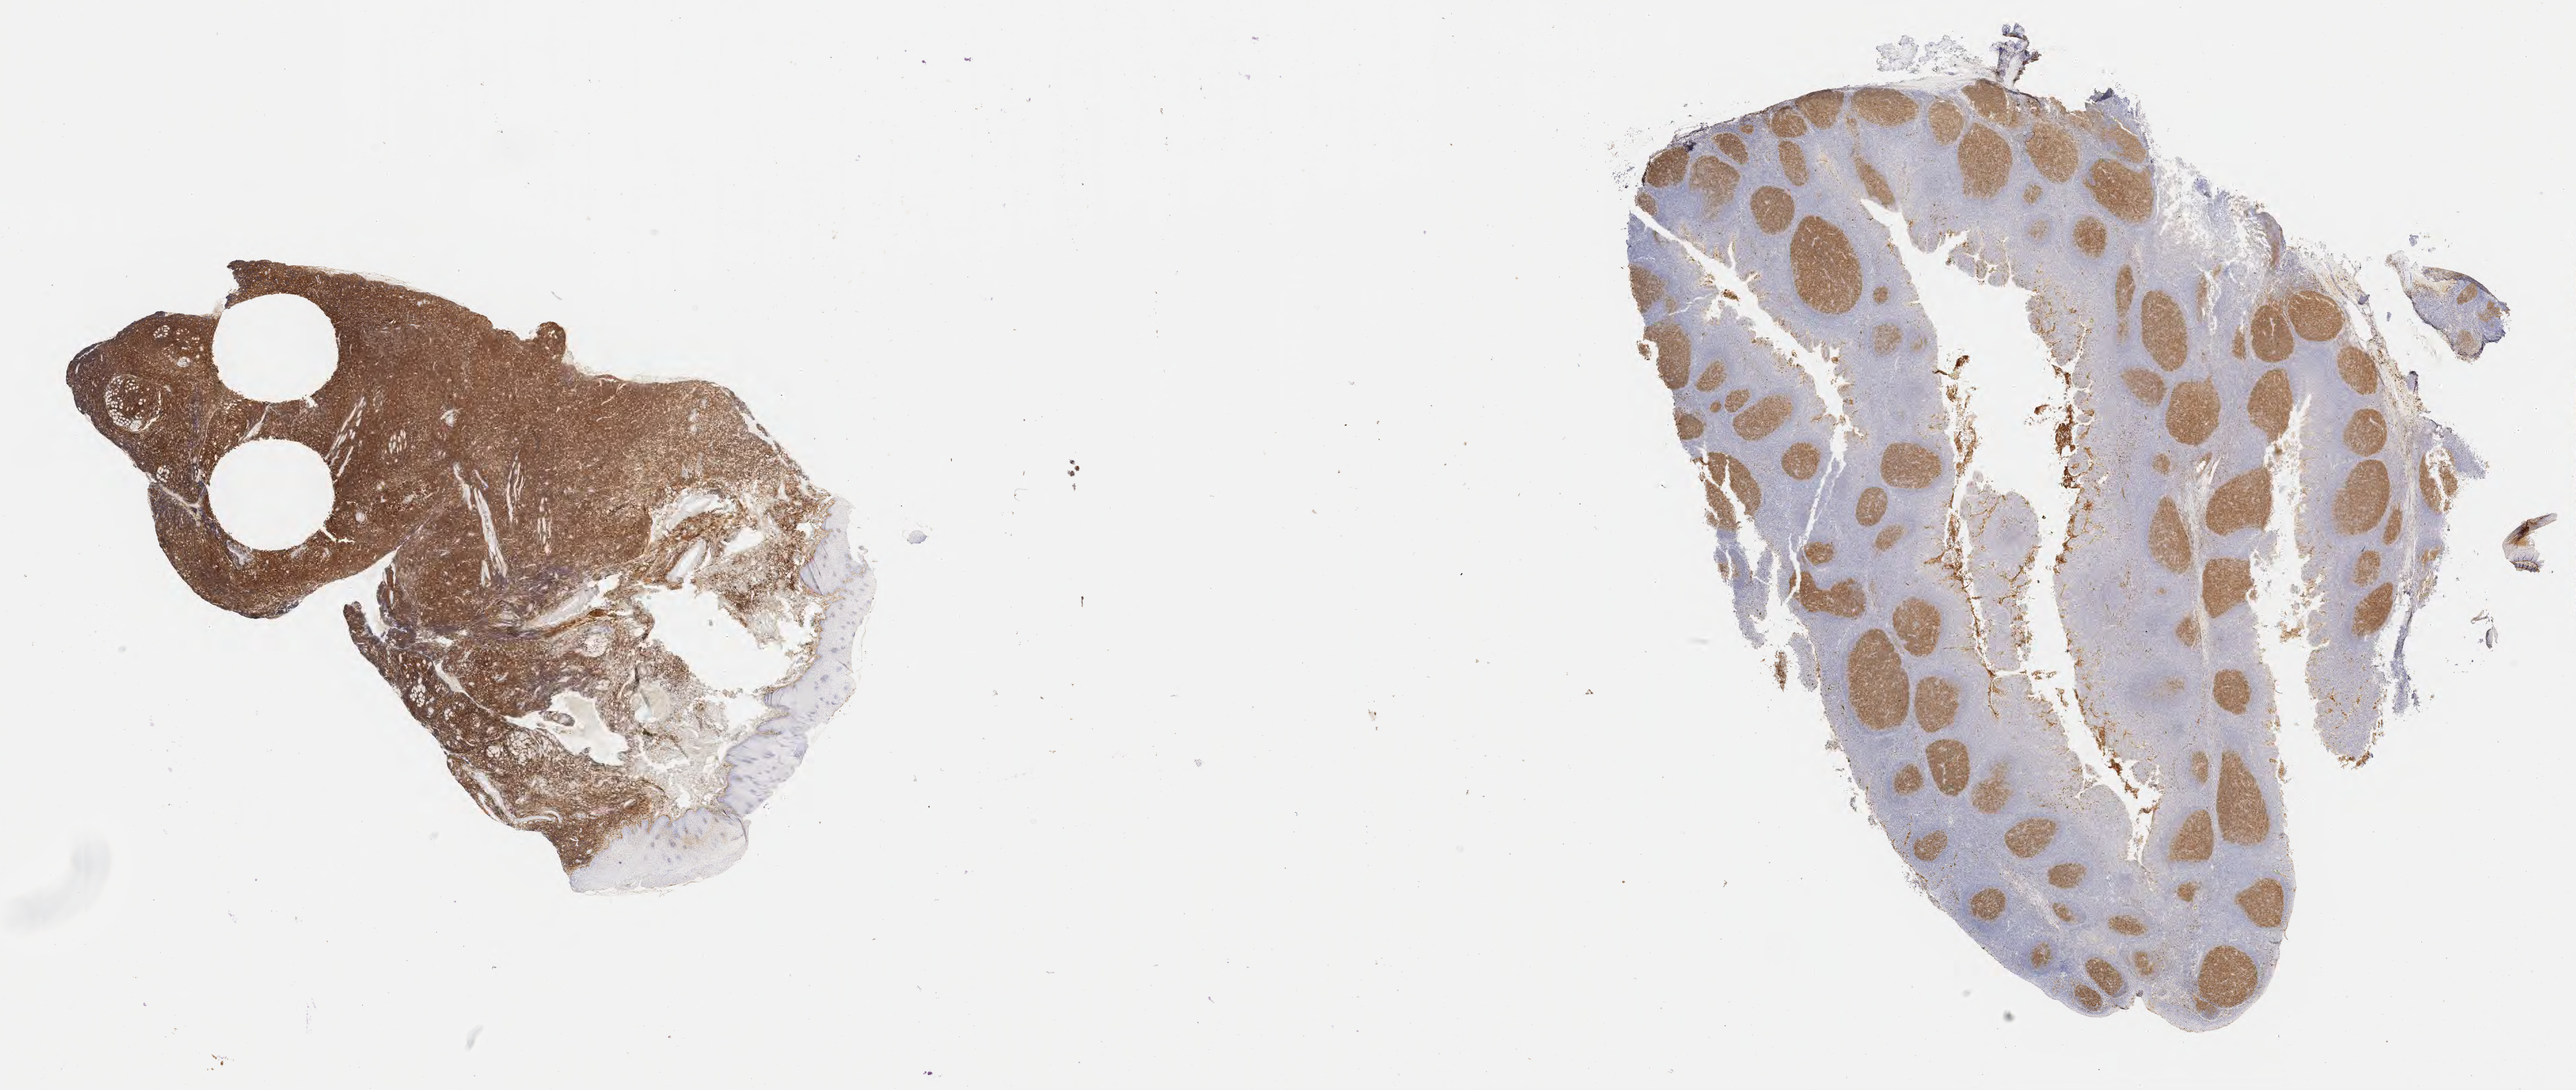
Immunohistochemistry (IHC) whole-slide image stained for CD10, whole scanned area (about 30.7 x 13.0 mm) shown as a low-resolution overview. Tumor tissue. Site: cranium. Male, age 6 years at initial diagnosis.
* diagnosis: Burkitt lymphoma, NOS